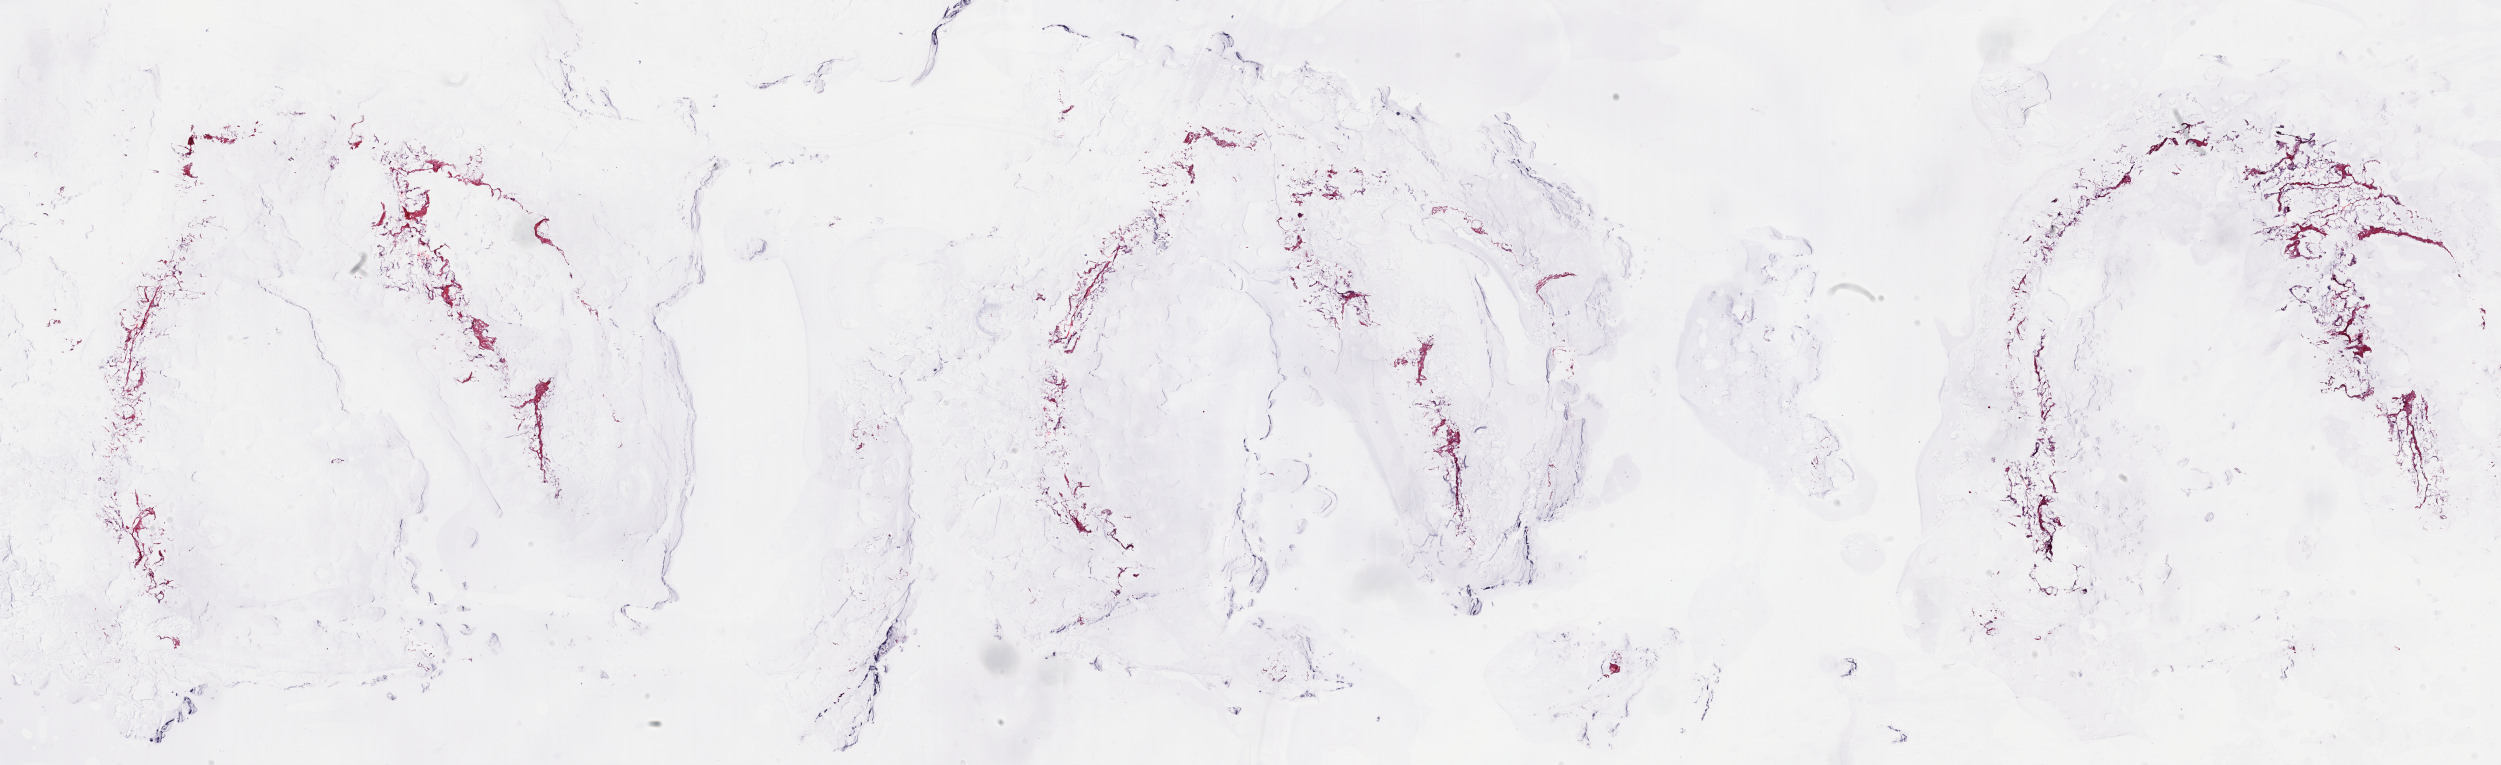
Digitized Hematoxylin and eosin (H&E) stained tissue section (whole slide), shown as a low-resolution overview of the whole scanned area (about 39.7 x 12.1 mm), frozen section from the top of the tissue portion, breast, solid tissue normal (non-tumour tissue) sample. Female, age 84 years at initial diagnosis. Composition of this section per pathologist review: tumour cells 0%, tumour nuclei 0%, normal cells 100%, stromal cells 0%, necrosis 0%. Inflammatory infiltration, as recorded: lymphocyte infiltration 1%, monocyte infiltration 0%, neutrophil infiltration 0%.
* this section: solid tissue normal sample (biorepository sample class)
* patient diagnosis: Infiltrating duct carcinoma, NOS